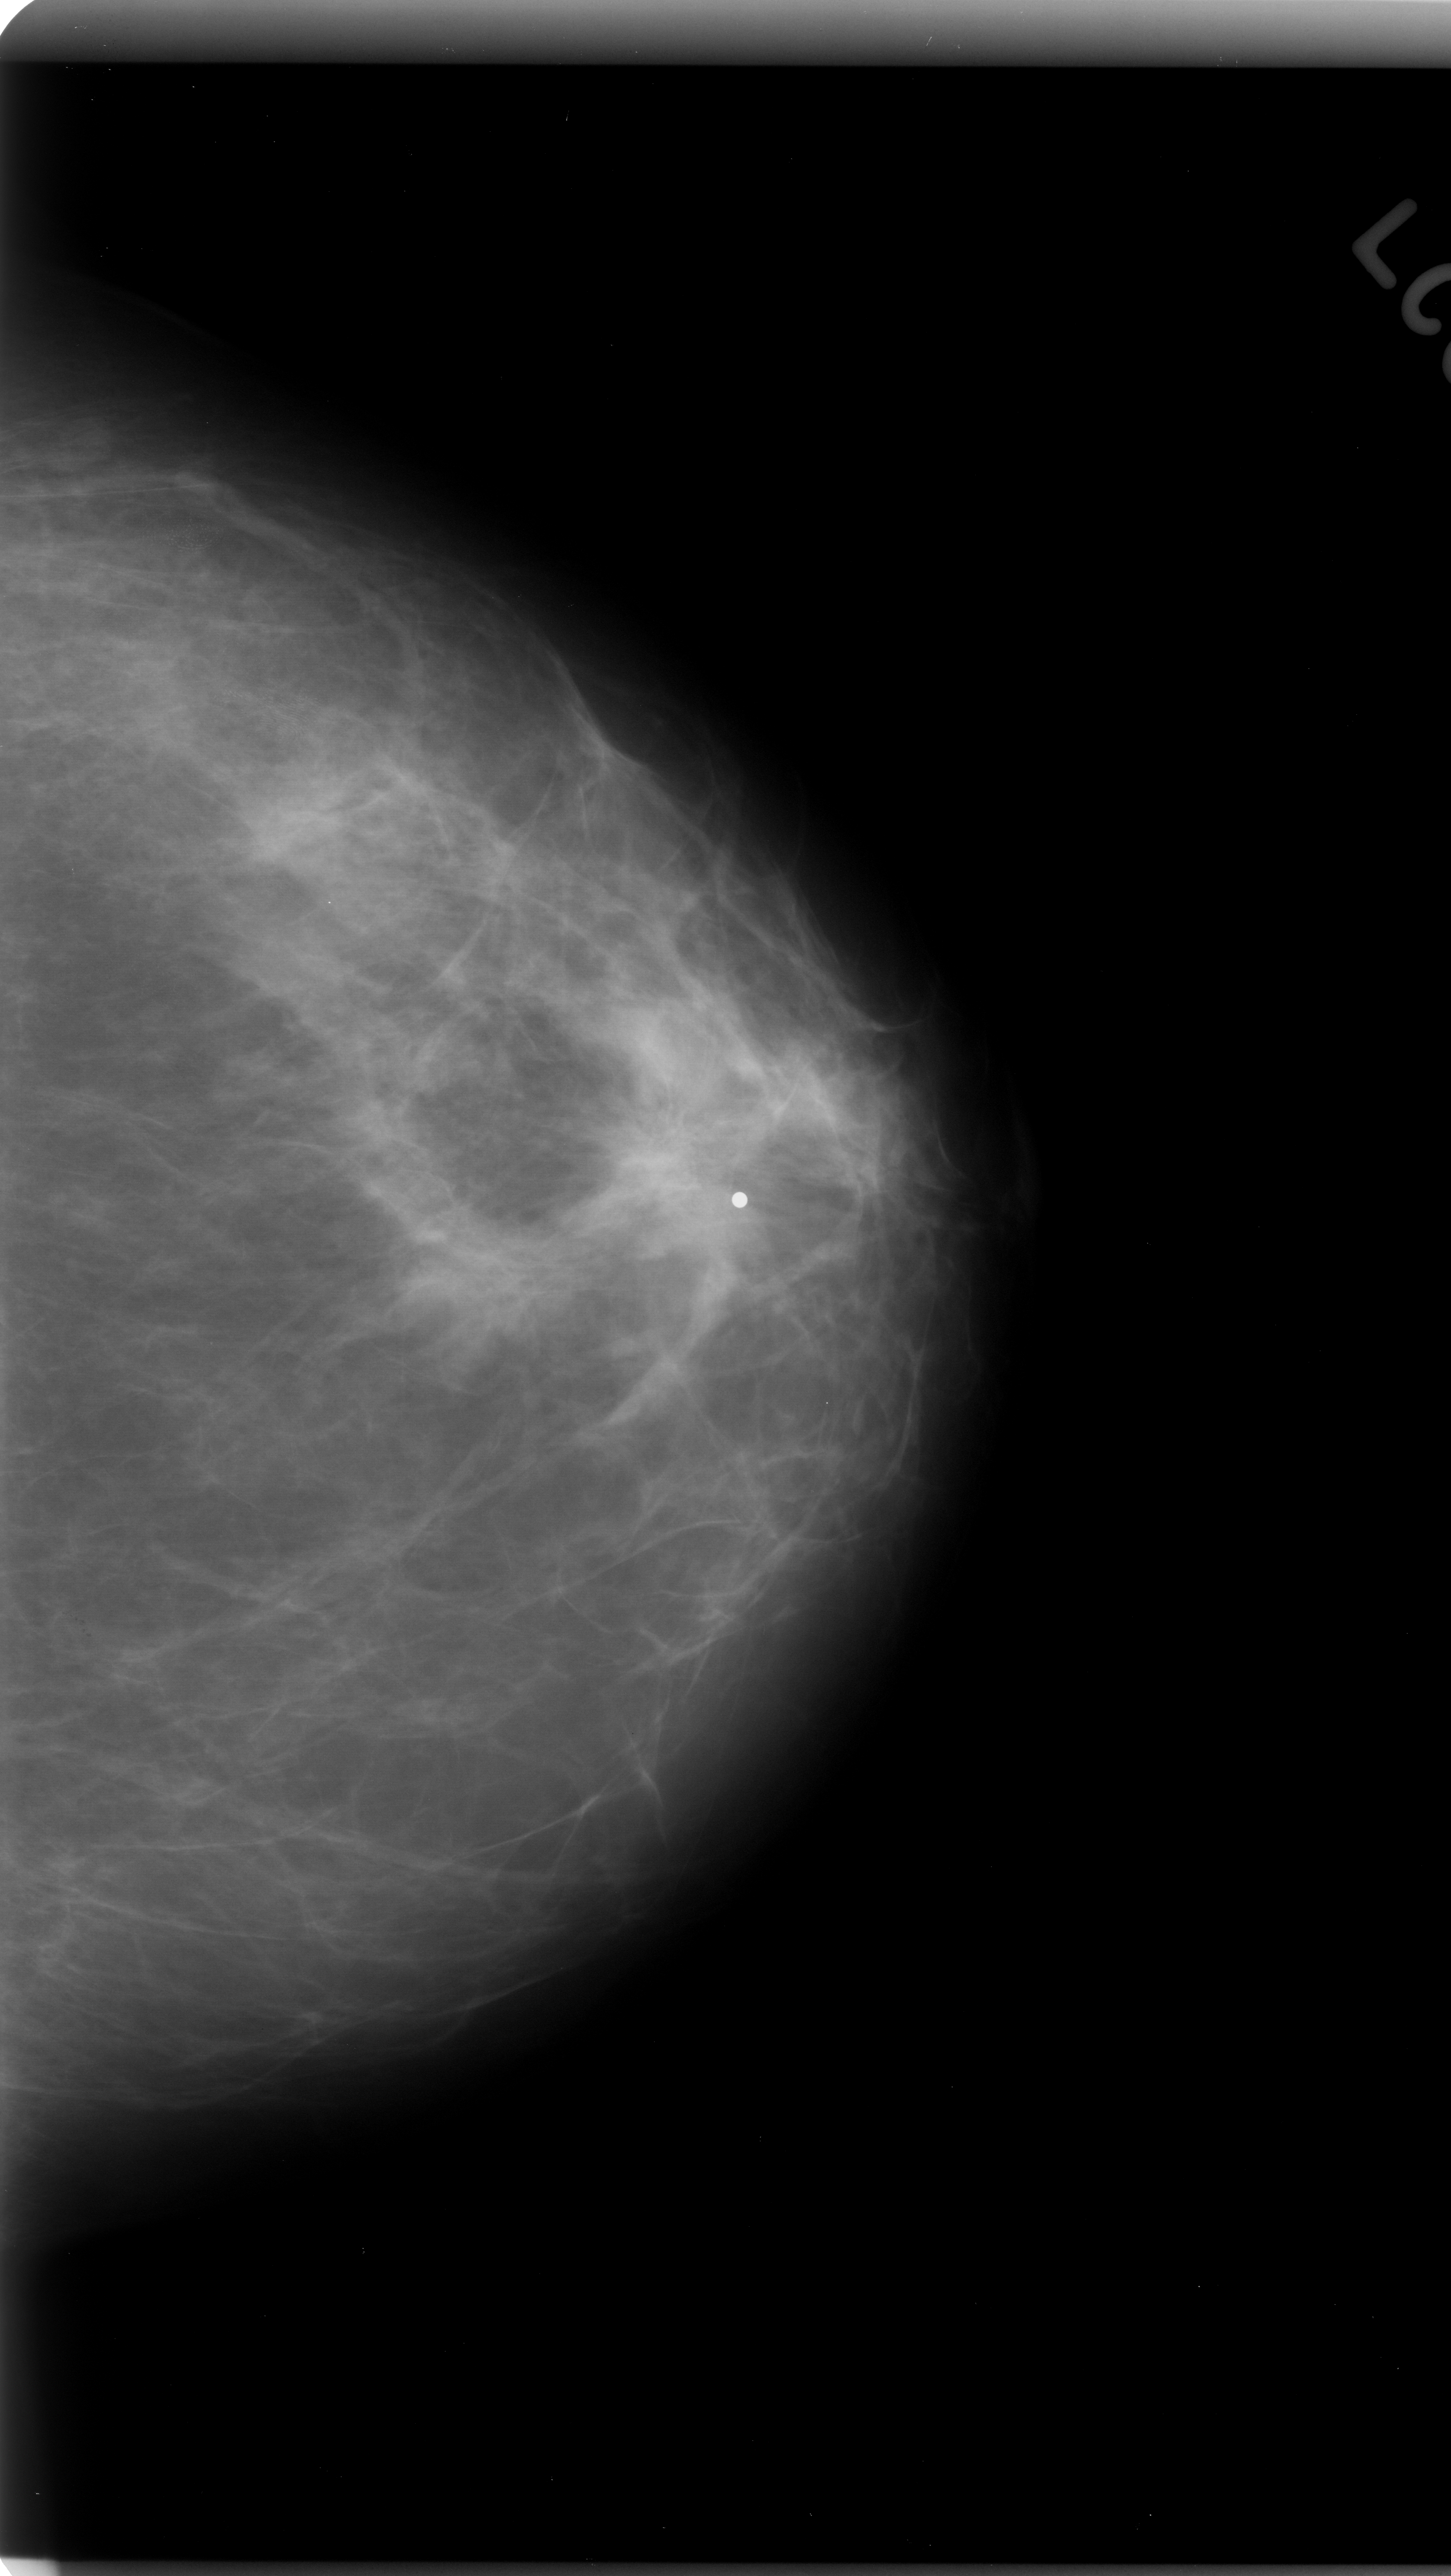
Scanned film-screen mammogram. Left breast. Craniocaudal (CC) view. BI-RADS breast density category 2 (scale 1–4). 1451 × 2576 image matrix.
Expert-marked regions of interest on this image (one box per marked abnormality):
- mass, shape architectural distortion, margins spiculated; BI-RADS assessment category 5; subtlety rating 5 on a 1 (subtle) to 5 (obvious) scale; pathology (as recorded): malignant: bounding box <590,1110,751,1225> (left, top, right, bottom; pixels)